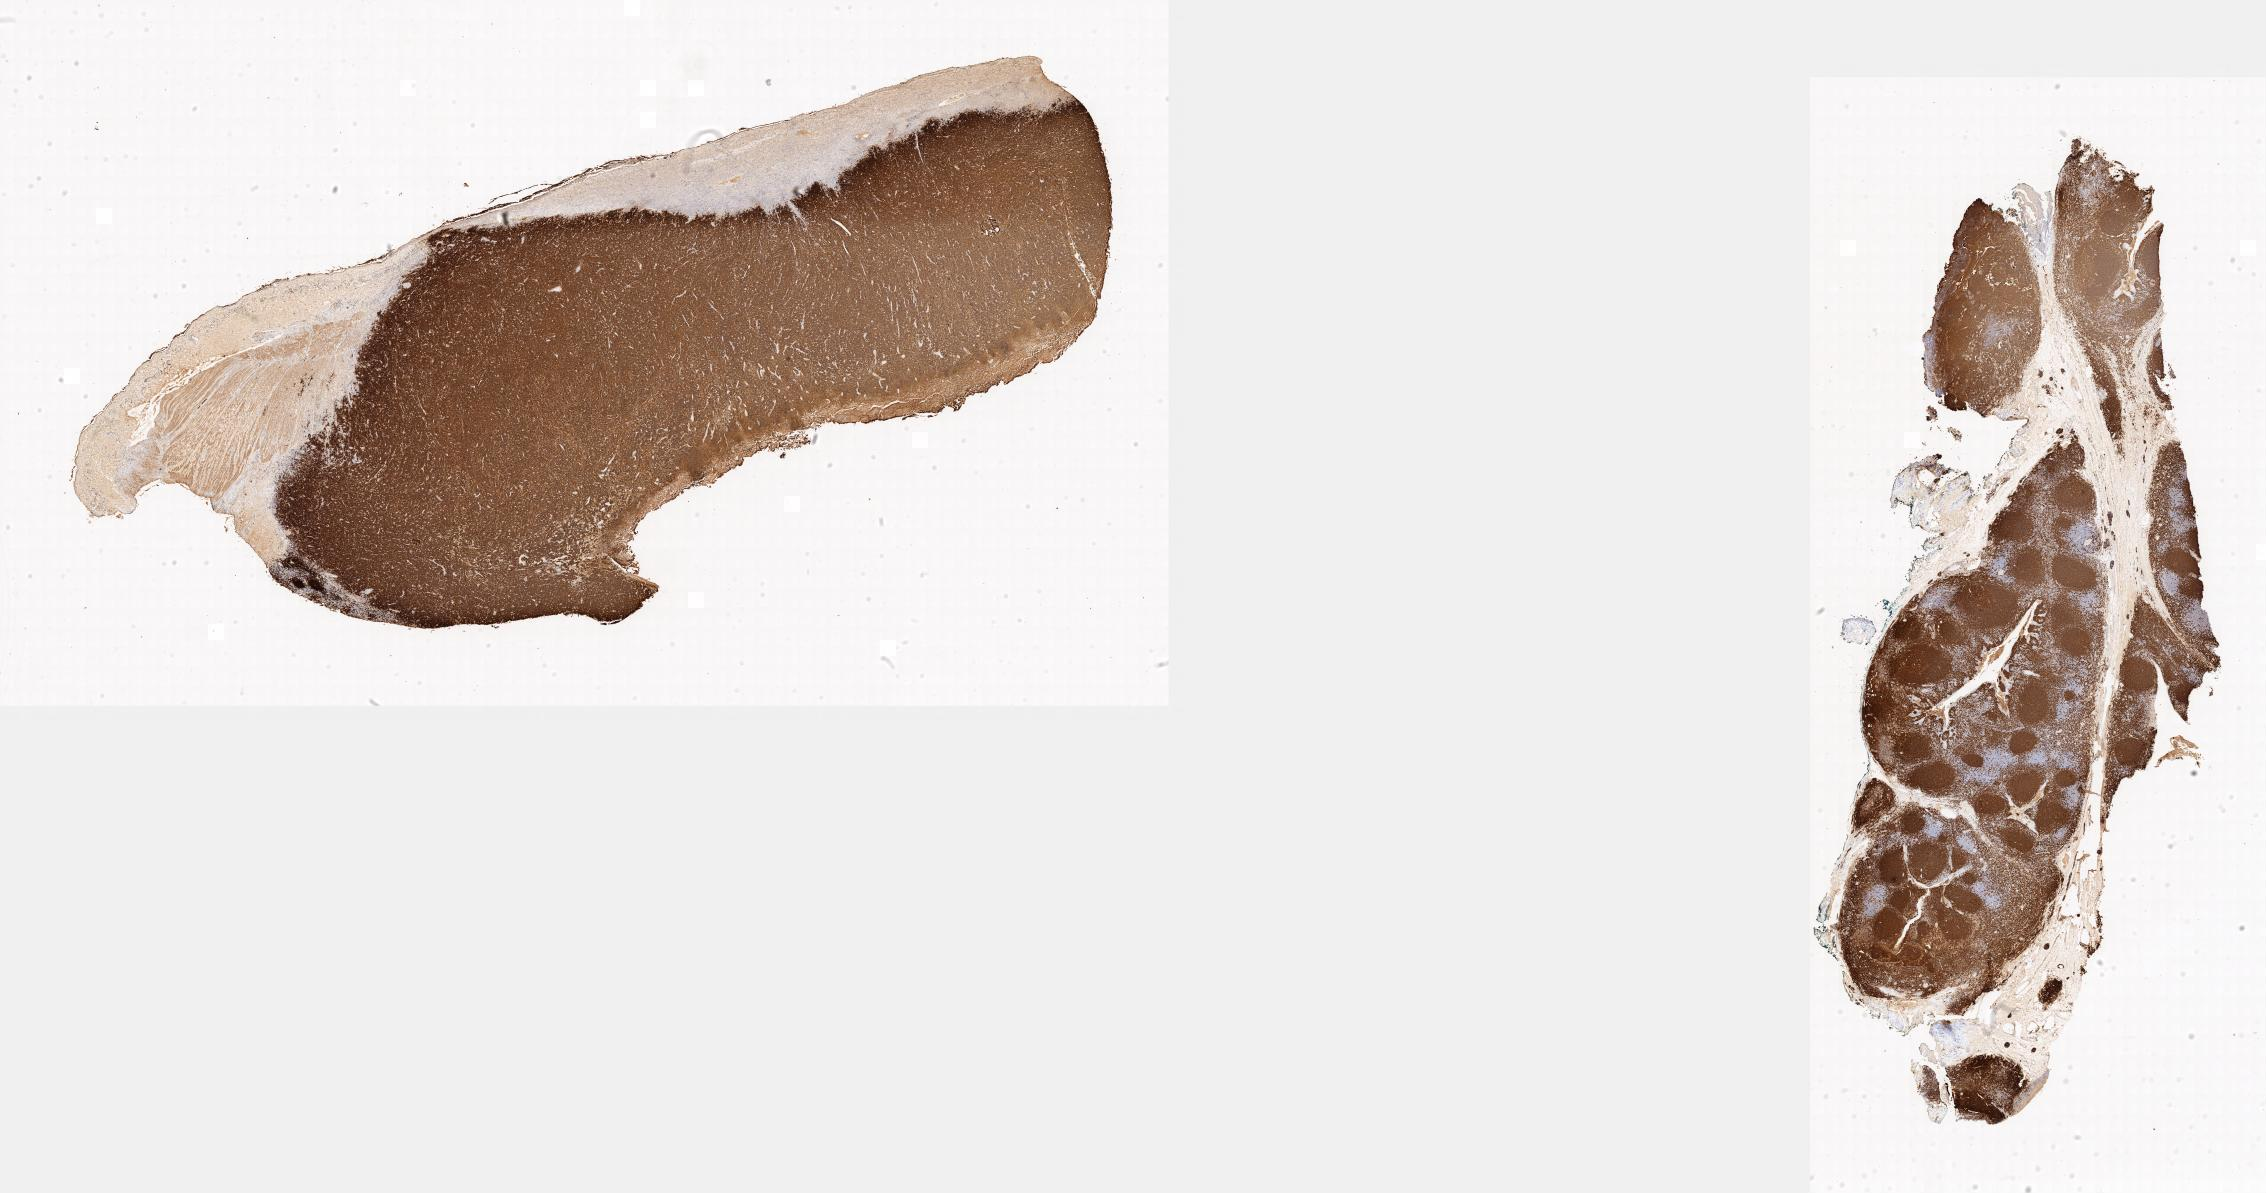
Whole-slide image, immunohistochemical stain for CD20, low-resolution overview of the scanned area; specimen: tumor tissue; anatomic site: small intestine. Male patient; age at initial diagnosis 3 years.
• diagnosis: Burkitt lymphoma, NOS